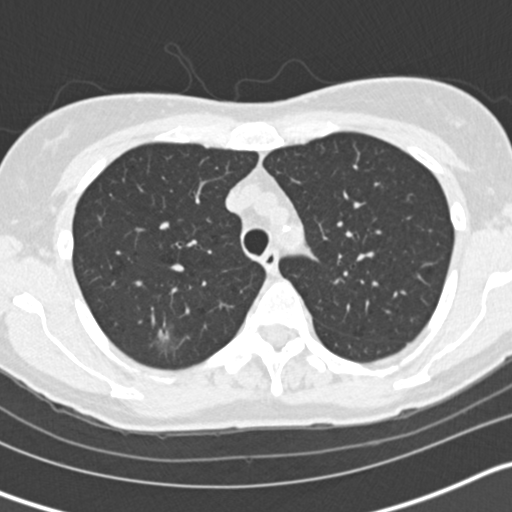
Low-dose screening chest CT, axial slice. Second screening round (one year after baseline). Lung window (W 1500 / L -600 HU). 2 mm slice thickness. 120 kVp. Female, age 58 years at enrolment. Current smoker at enrolment.
• Expert reader's lesion annotation, bounding box [x1, y1, x2, y2] px = [135, 319, 192, 365].
• The screening reader recorded 3 non-calcified nodules or masses ≥4 mm on this exam (right upper lobe, left upper lobe, left lower lobe); which of them this box marks is not recorded.
• Official screen result: positive, other.
• Lung cancer was diagnosed 59 days after this screen: bronchiolo-alveolar adenocarcinoma, NOS, right upper lobe, moderately differentiated (G2), stage IA (AJCC 6th edition), 7 mm at pathology.